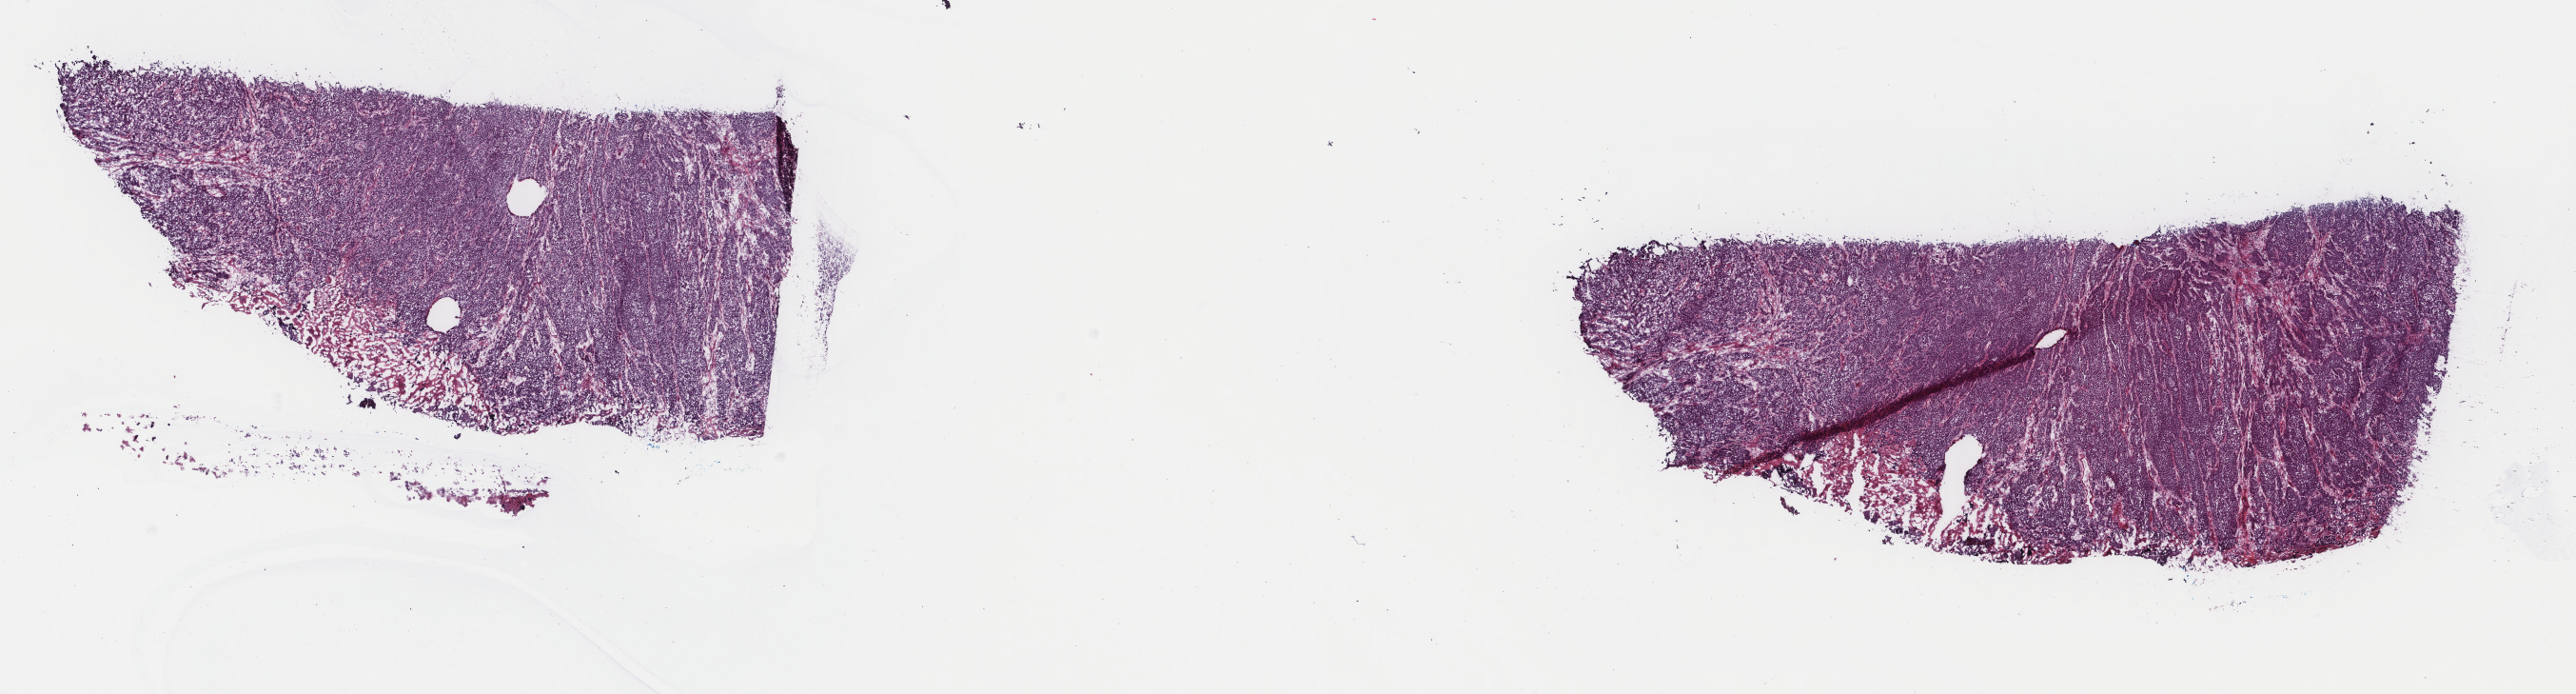
Whole-slide histology image, H&E-stained, whole scanned area (about 21.5 x 5.8 mm, acquisition: 40x scan) shown as a low-resolution overview. Frozen section from the top of the tissue portion. Bladder, primary tumour sample. Patient: male, age at initial diagnosis 54 years. Histologic grade: high grade. Composition of this section per pathologist review: tumour cells 100%, tumour nuclei 90%, normal cells 0%, stromal cells 0%, necrosis 0%. Inflammatory infiltration, as recorded: lymphocyte infiltration 1%, monocyte infiltration 0%, neutrophil infiltration 0%.
Diagnosis: Transitional cell carcinoma. AJCC pathologic stage: III (7th edition). Lymph nodes positive (case pathology): 0 of 9 examined.